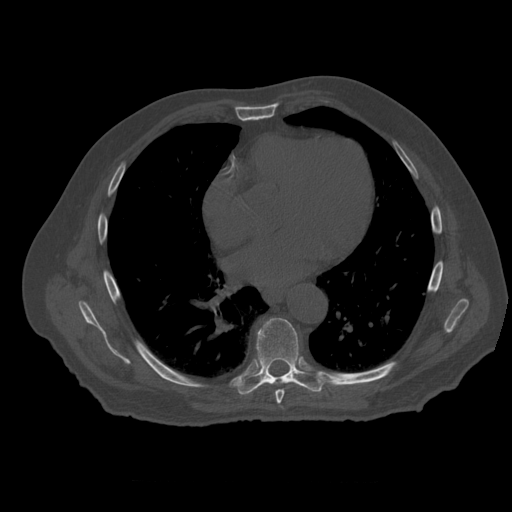
CT including the spine, one axial slice. Slice 347 of 399 in the series (ordered by position). Bone window (W 1800 / L 400 HU). 512 × 512 image matrix. Patient age 73 years. Case-level facts recorded for this patient, not image findings: primary cancer: prostate; vertebrae with lytic lesions (as recorded): L2.
Annotated regions visible in this slice (semi-automatically segmented with operator editing):
- T7 vertebra: bounding box (x1, y1, x2, y2) in pixels: (276, 390, 285, 409)
- T8 vertebra: (236, 318, 324, 395)